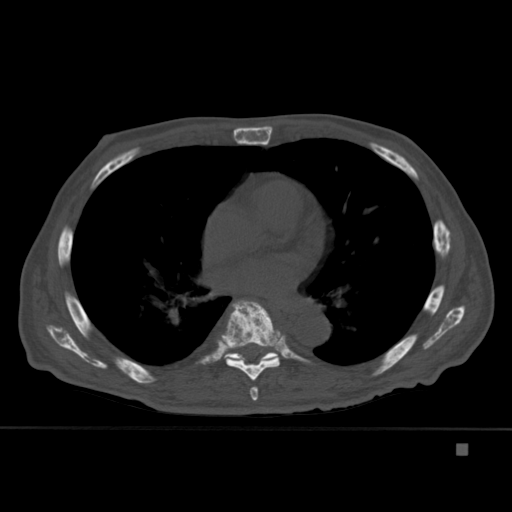
CT including the spine, one axial slice. Slice 276 of 451 in the series (ordered by position). Bone window (W 1800 / L 400 HU). 1.5 mm slice thickness. 512 × 512 image matrix, field of view 378 × 378 mm. Male patient, age 75 years. Case-level facts recorded for this patient, not image findings: primary cancer: prostate.
Structures marked on this image (semi-automatic segmentation, software-assisted and operator-edited):
- T6 vertebra: bounding box [x1, y1, x2, y2] px = [249, 386, 258, 401]
- T7 vertebra: [221, 300, 286, 381]
- T8 vertebra: [224, 306, 278, 362]